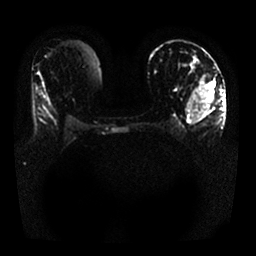
Breast MRI, one axial slice; position 14 of 25 along the scan axis; diffusion-weighted series; image 2 of 4 stored at this slice position (different b-values; order by instance number); 1.5 T; 4 mm slice thickness; 256 × 256 image matrix, field of view 340 × 340 mm. Female patient.
Annotated regions visible in this slice (manually delineated by an expert):
- tumour on diffusion-weighted imaging: bounding box (x1, y1, x2, y2) in pixels: (191, 82, 215, 121)